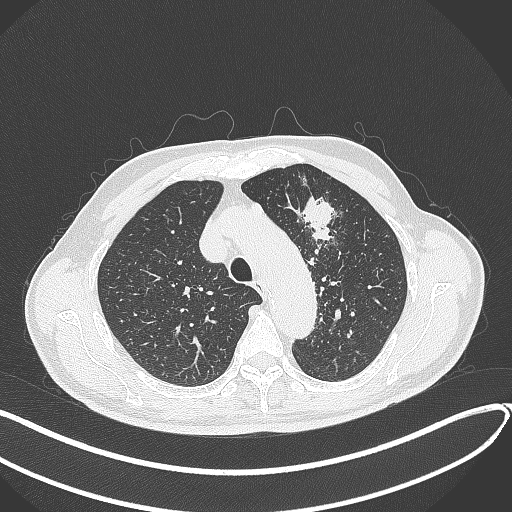
Chest CT, one axial slice; position 317 of 459 along the scan axis; reconstruction kernel B70f; lung window (W 1500 / L -600 HU); 512 × 512 image matrix, field of view 400 × 400 mm. Male patient, age 74 years. Case-level facts recorded for this patient, not image findings: clinical TNM (as recorded): T2b N0 M1c.
Outlined on this slice (bounding box drawn by a radiologist):
- lung tumour (recorded histology: adenocarcinoma): bounding box <298,191,345,247> (left, top, right, bottom; pixels)